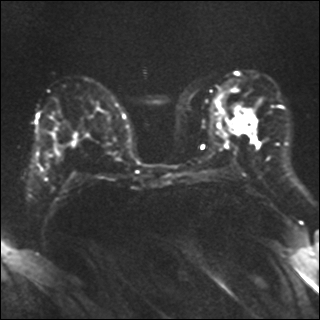
Breast MRI, one axial slice; slice 20 of 40 in the series (ordered by position); diffusion-weighted series; image 2 of 4 stored at this slice position (different b-values; order by instance number); 1.5 T; 4 mm slice thickness; 320 × 320 image matrix, field of view 320 × 320 mm. Female patient.
Outlined on this slice (outlined manually by an expert reader):
- tumour on diffusion-weighted imaging: box from (x=233, y=106) to (x=253, y=135) px